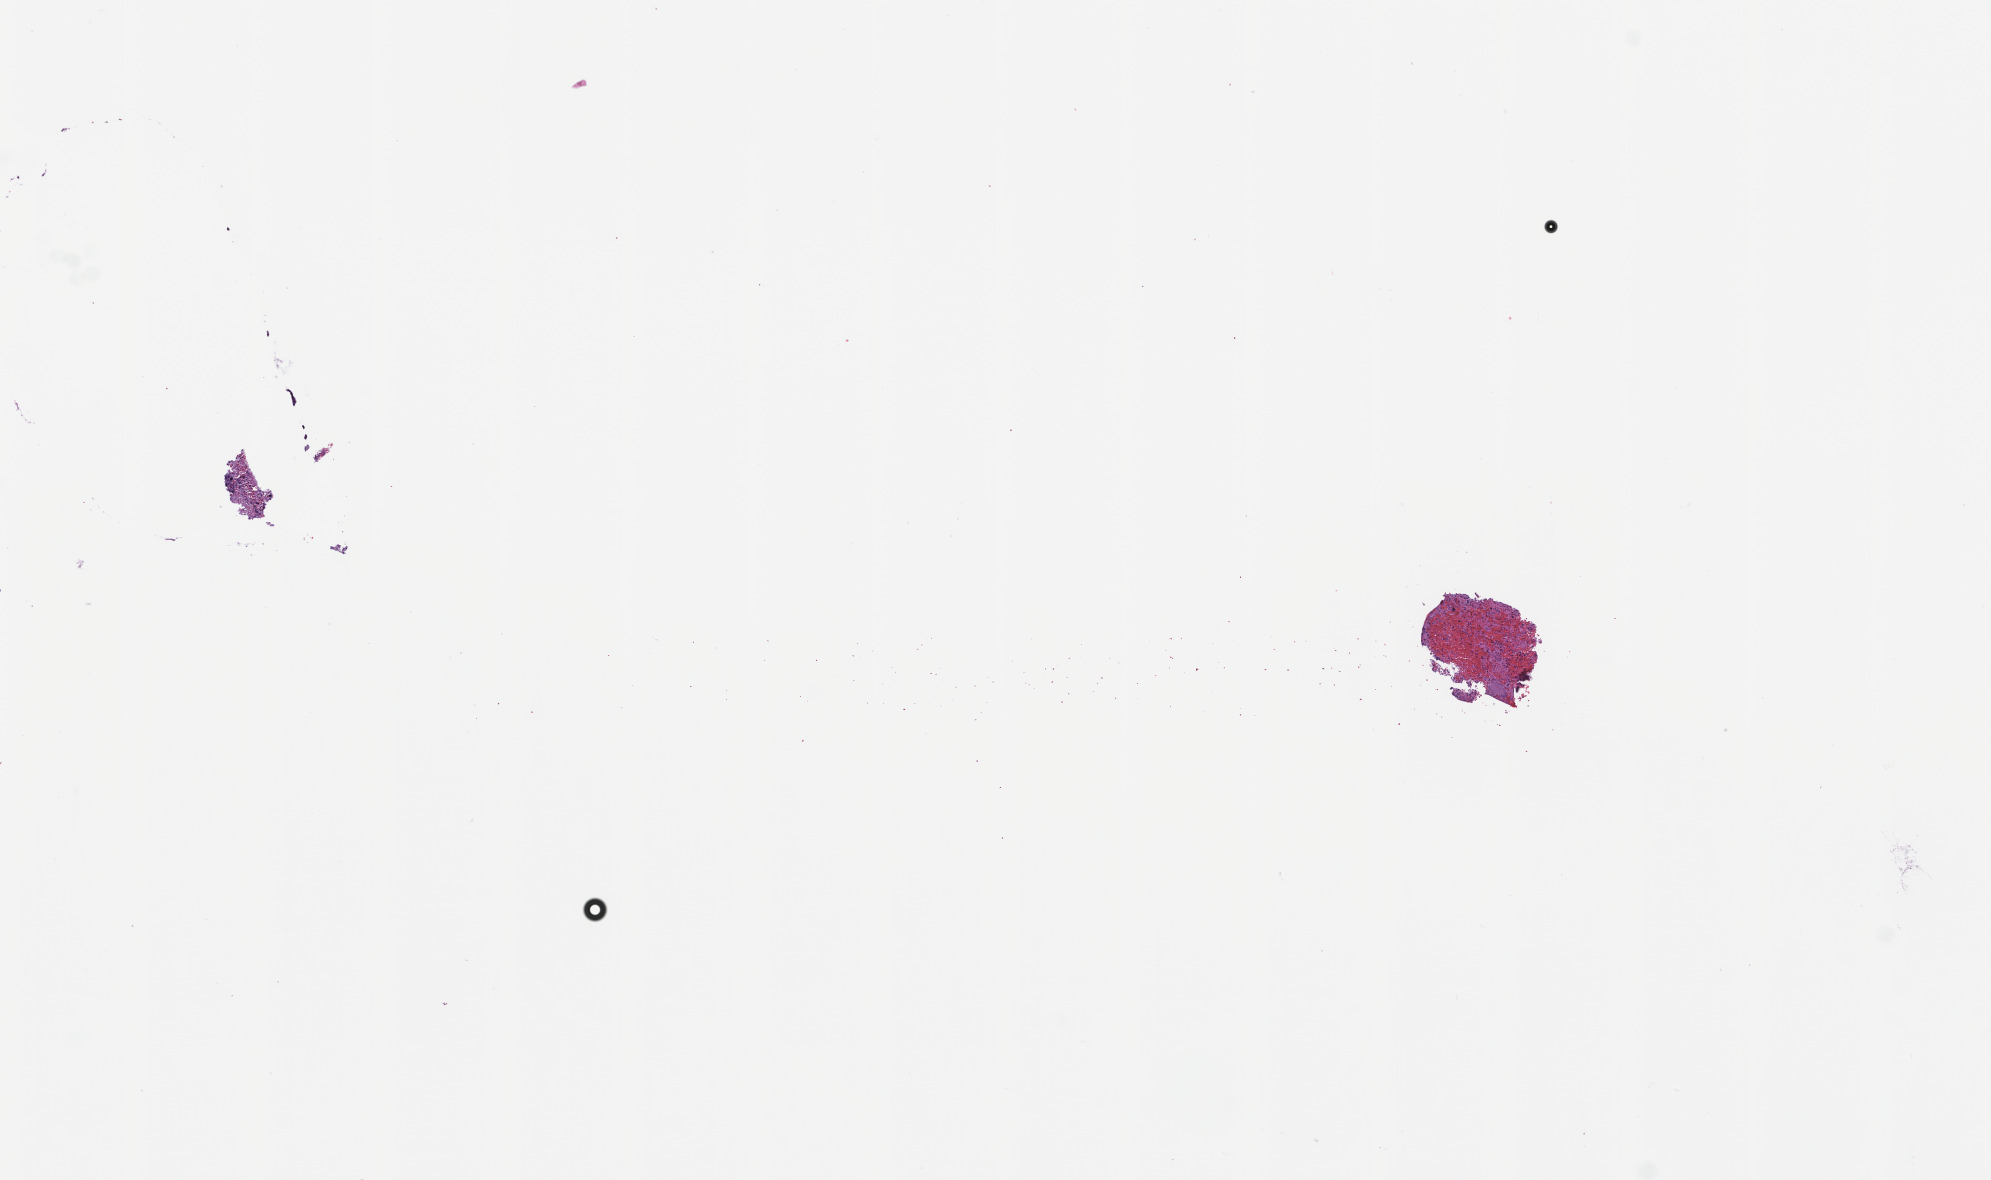
Digitized hematoxylin and eosin (H&E)-stained section, low-resolution overview of the scanned area, about 8.0 x 4.8 mm, FFPE section, tissue site: lung, collected at baseline (before treatment). Patient: male.
* this section: primary tumour tissue
* diagnosis: Non-Small Cell Lung Carcinoma